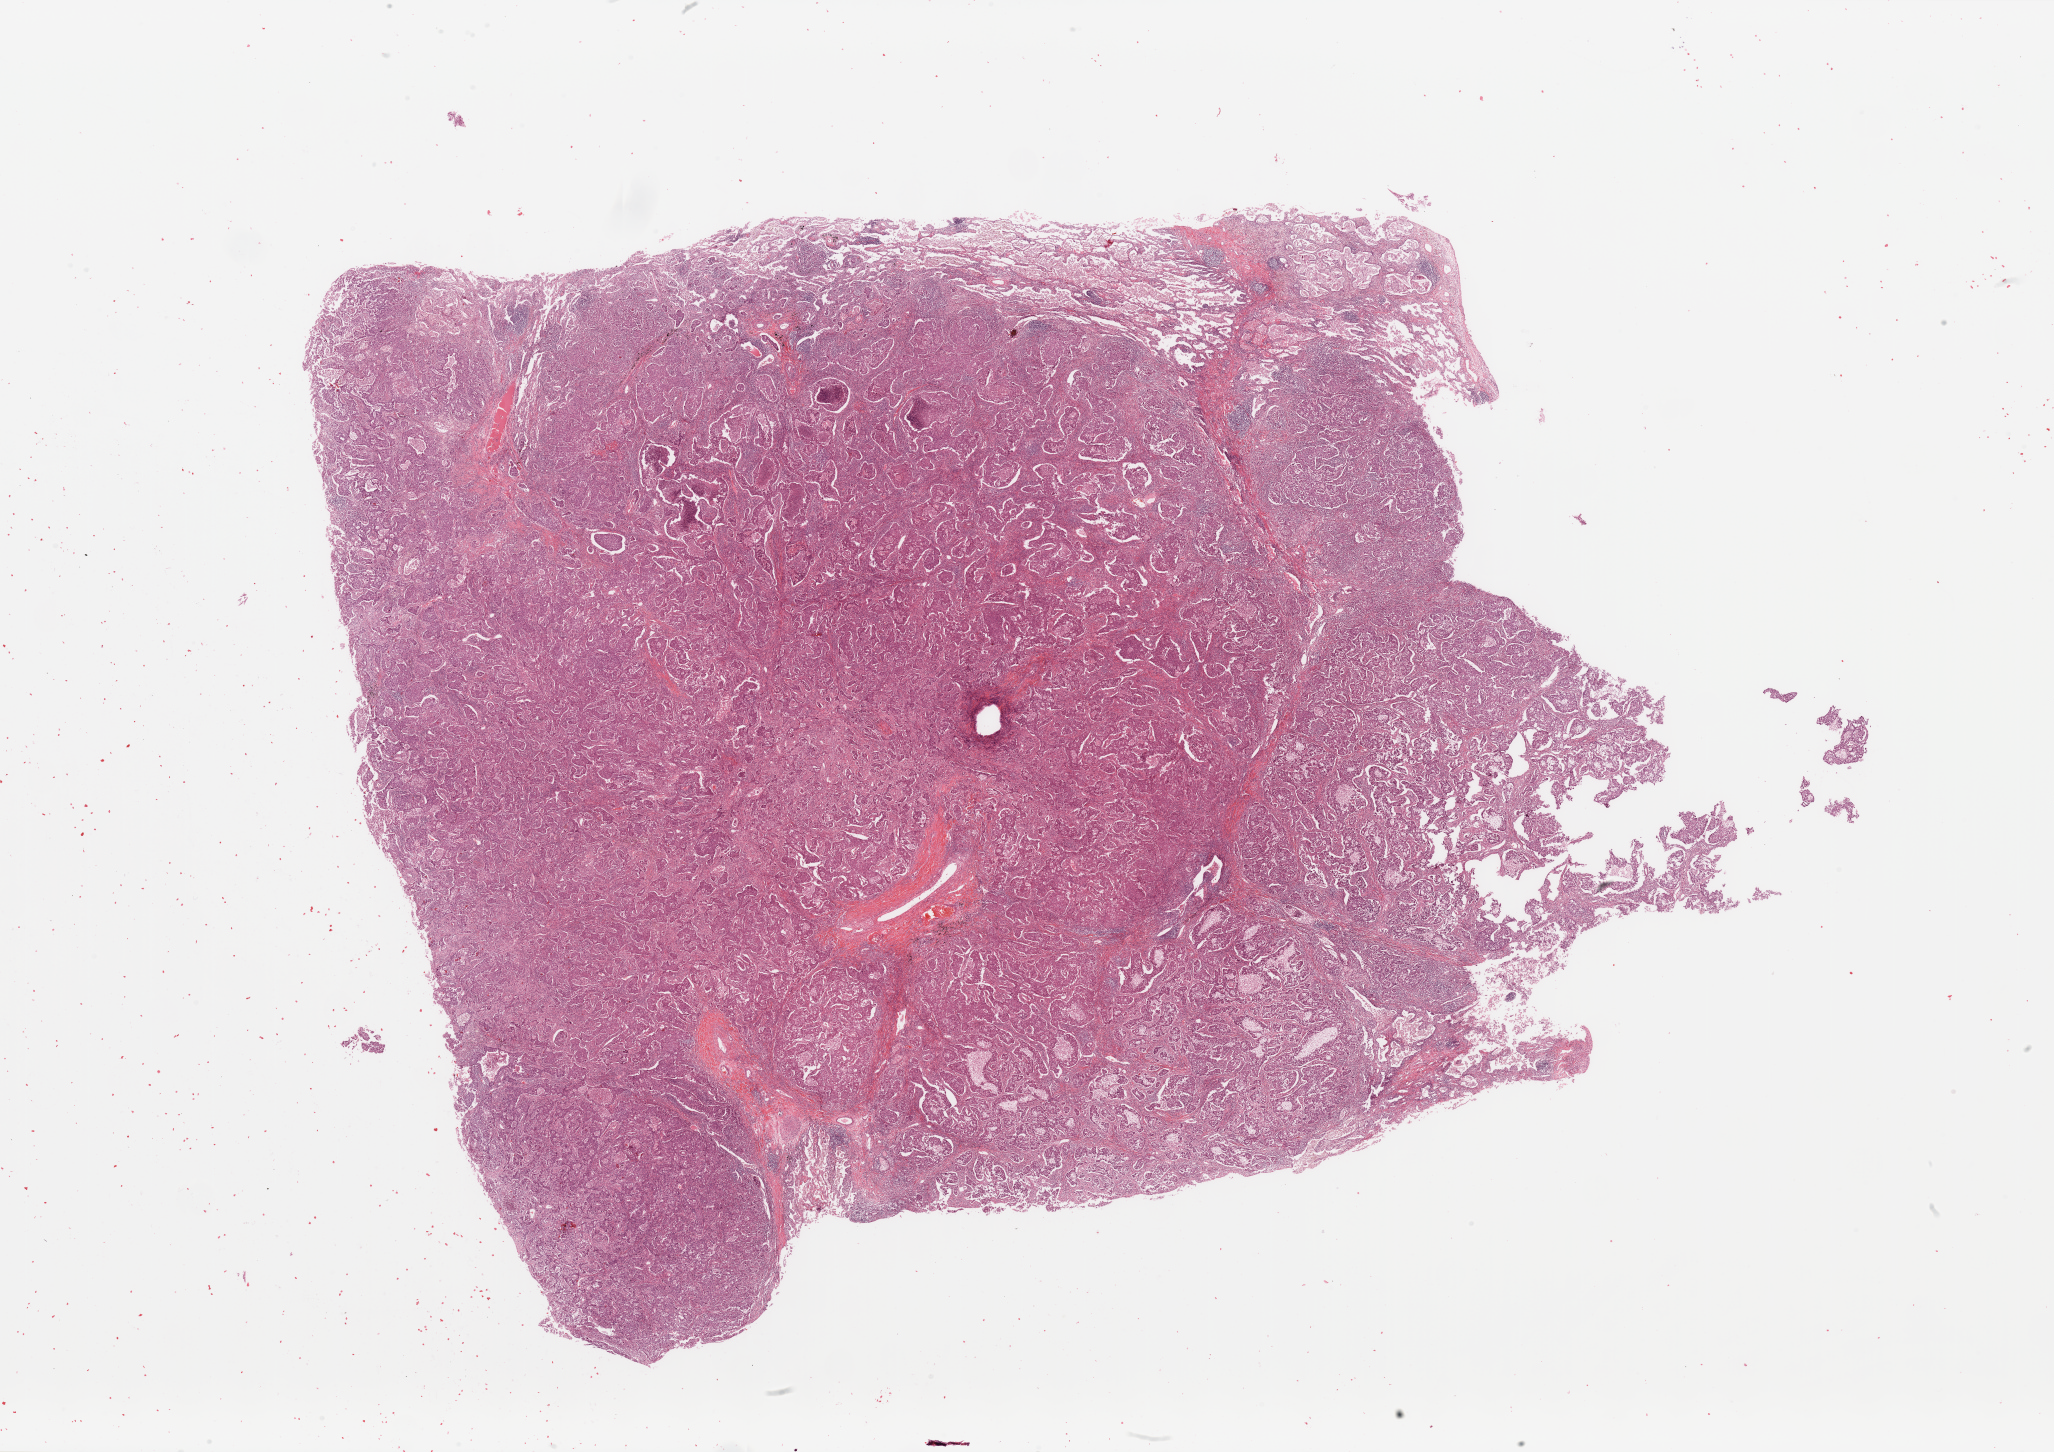
Digitized H&E-stained tissue section (whole slide) — shown as a low-resolution overview of the whole scanned area (about 32.5 x 23.0 mm, acquisition: 20x scan); tumour tissue sample, sampled site: lung. Male, 49 y/o. Histologic grade: G3 (poorly differentiated). Pathologist review of this section (percent, as recorded): tumour nuclei 70%, necrosis 5%.
Histologic diagnosis: Adenocarcinoma, NOS. AJCC pathologic stage: IIB.